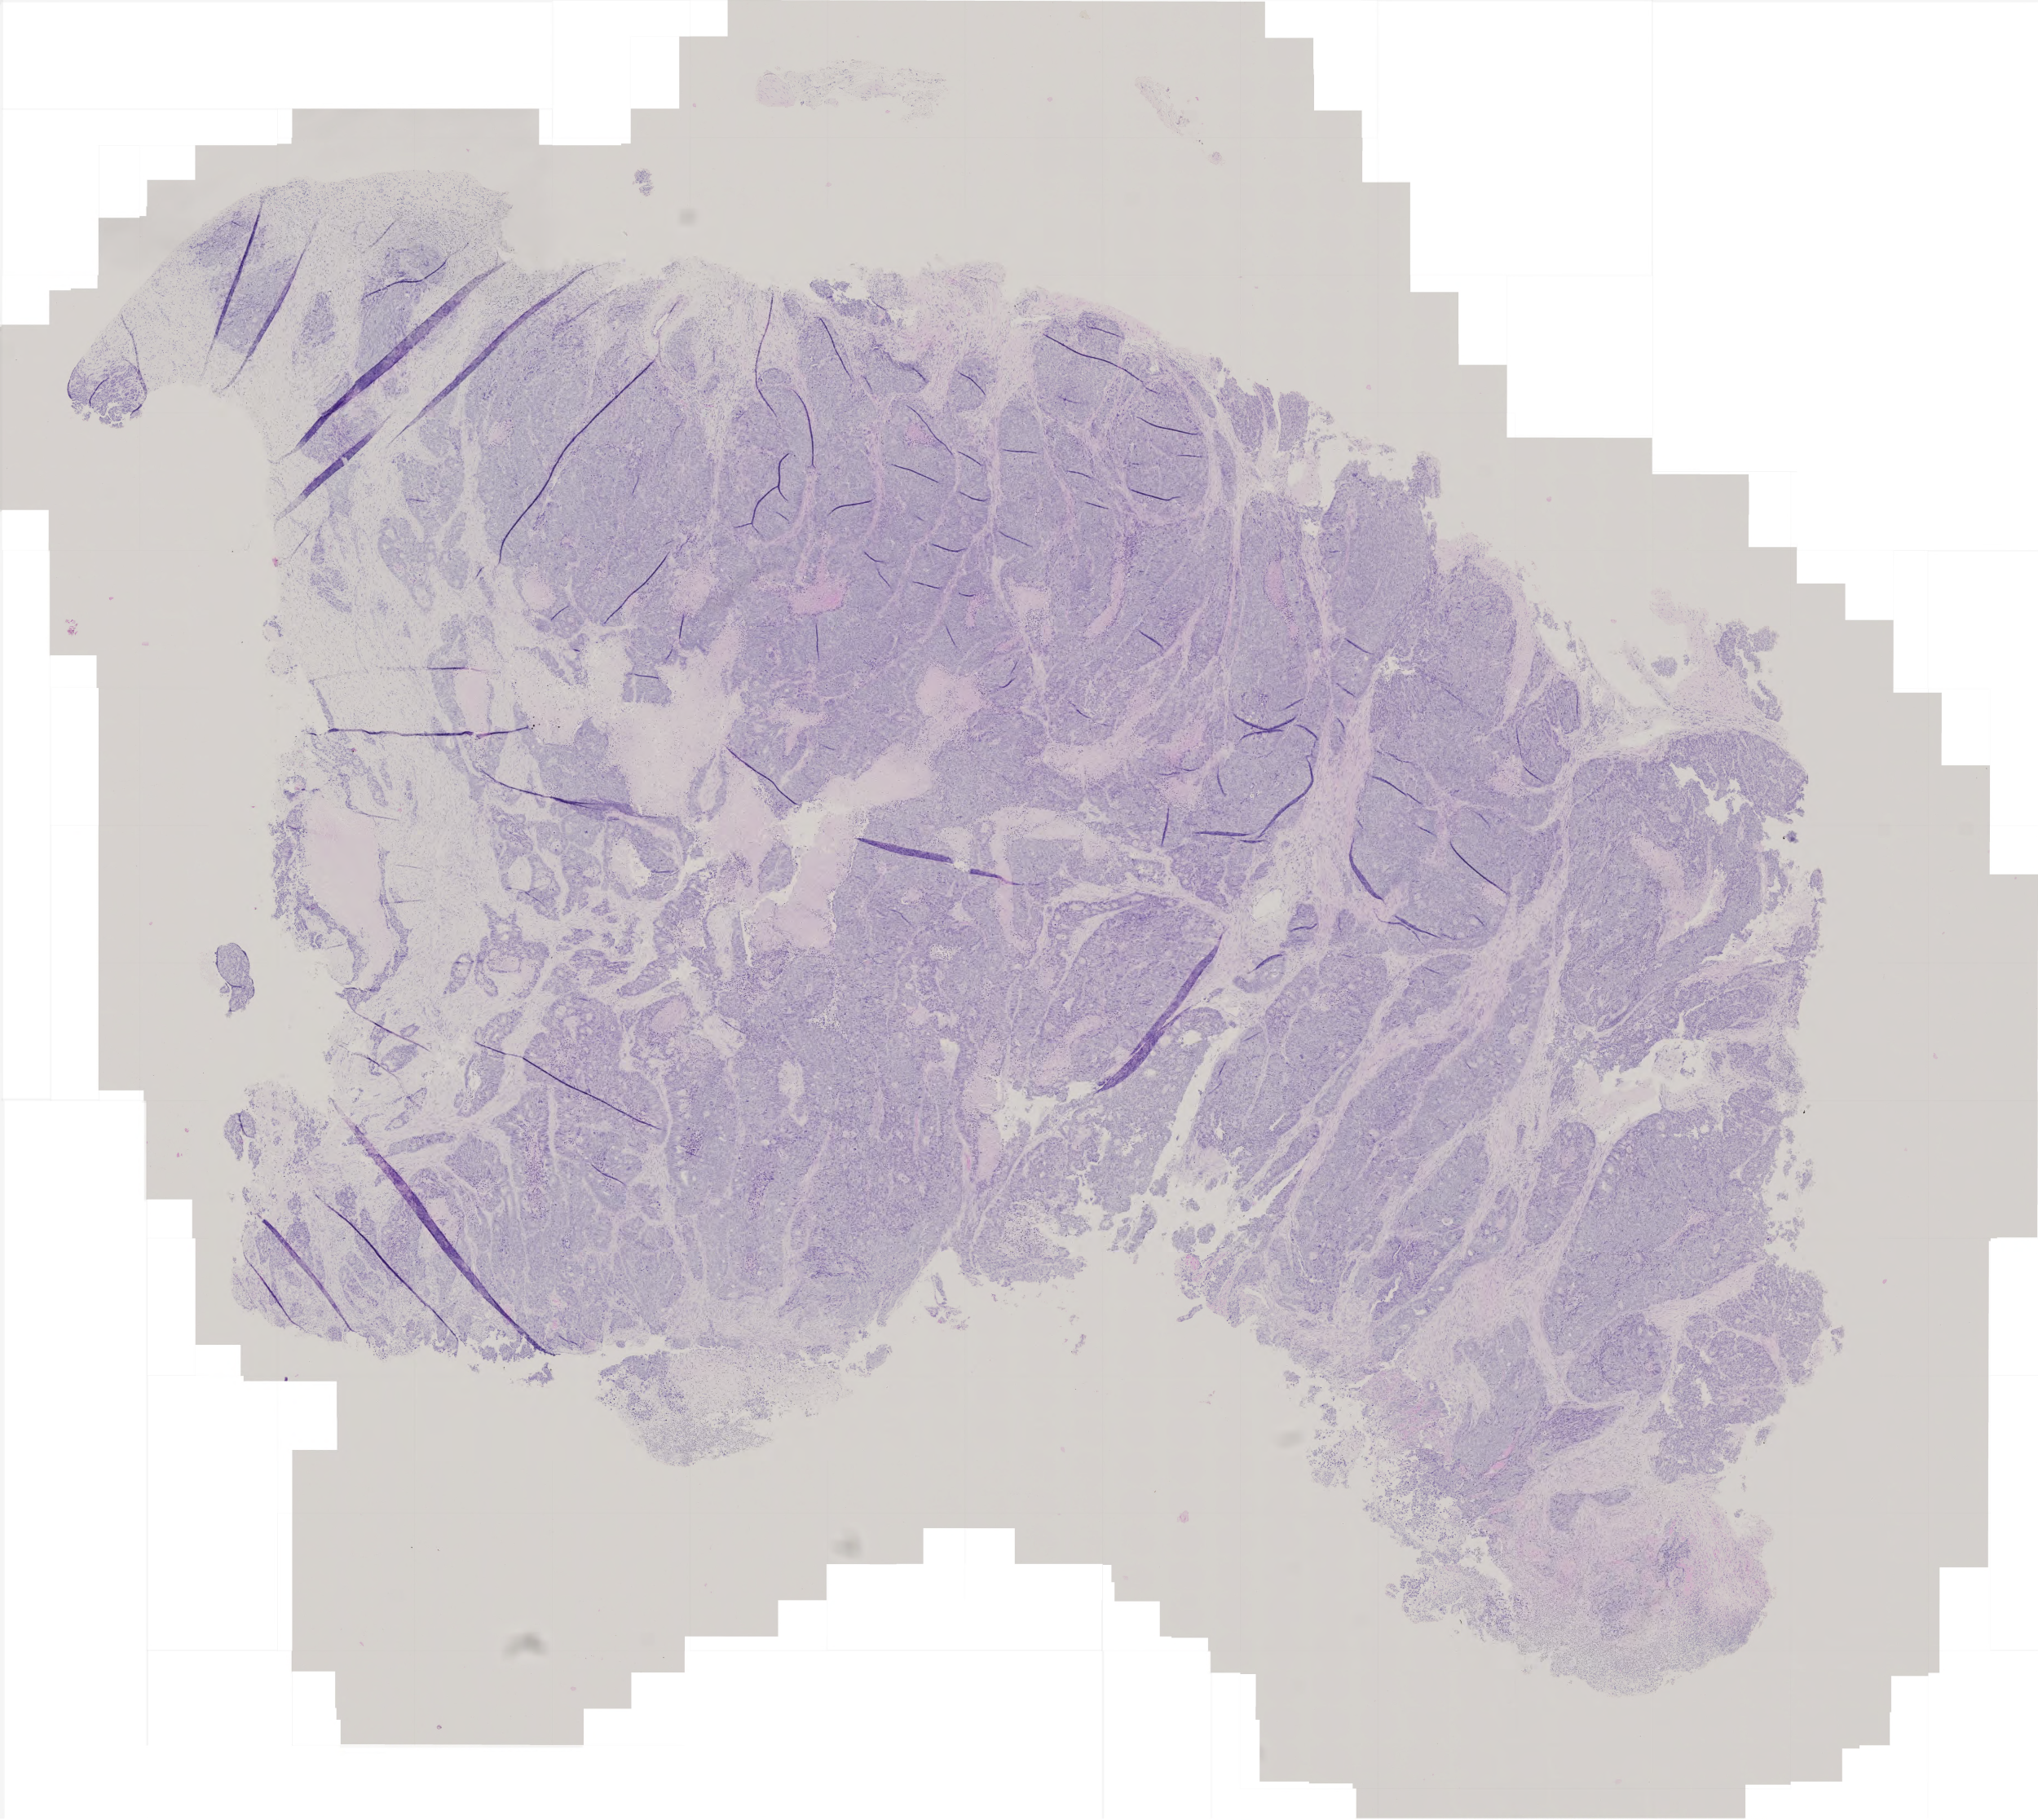
Whole-slide histology image, Hematoxylin and eosin (H&E) stained, shown as a low-resolution overview of the whole scanned area (about 5.0 x 4.5 mm), FFPE section, stomach, primary tumour sample. Male, age 66 years at initial diagnosis. Histologic grade: G3 (poorly differentiated).
* AJCC pathologic stage: II
* TNM: T3 N0 M0
* pathologic diagnosis: Adenocarcinoma, intestinal type (body of stomach)